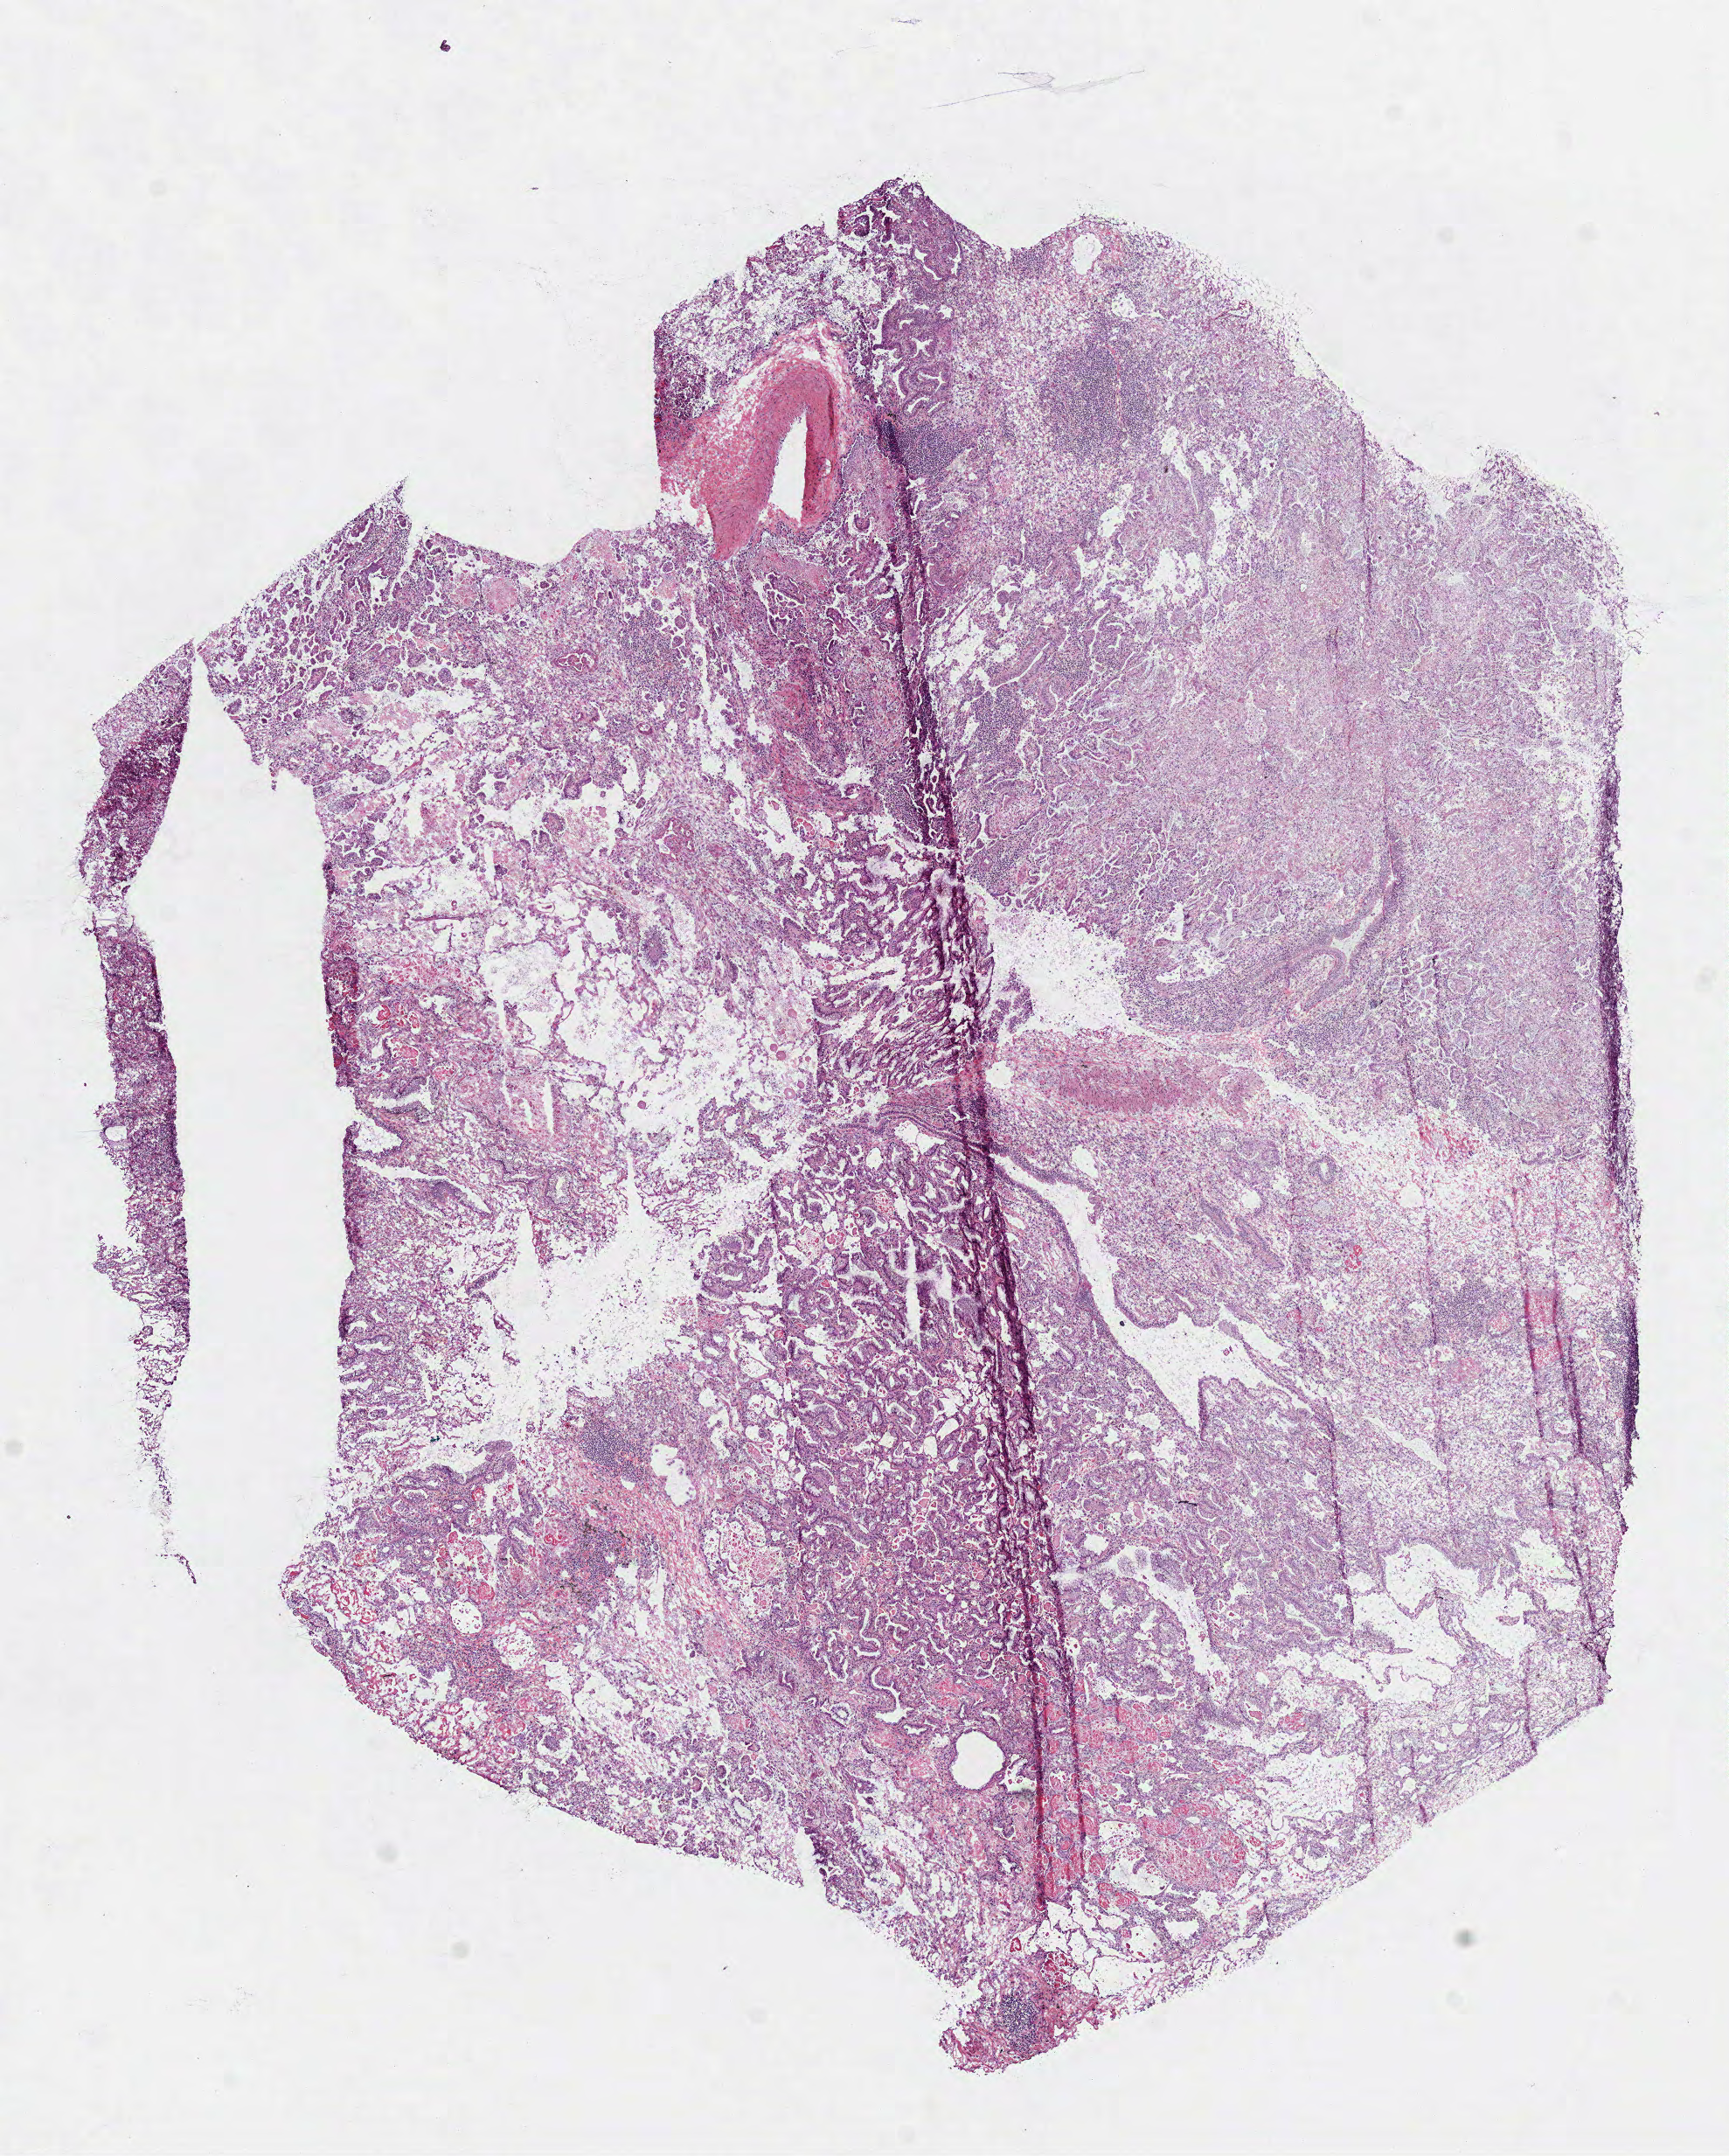
Digitized H&E tissue section (whole slide) — whole scanned area (about 8.0 x 9.9 mm) shown as a low-resolution overview, frozen section, primary tumour sample from the lung. Male patient. Composition of this section per pathologist review: tumour cells 70%, tumour nuclei 60%, normal cells 10%, stromal cells 15%, necrosis 5%.
• diagnosis: Adenocarcinoma, NOS (lower lobe, lung)
• TNM: T3 N0 M0
• AJCC pathologic stage: IIB